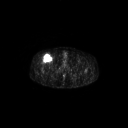
FDG PET of an extremity soft-tissue mass (from a PET/CT study), one axial slice. Slice 303 of 311 in the series (ordered by position). 3.27 mm slice thickness. 128 × 128 image matrix, field of view 700 × 700 mm. Male patient, age 56 years. Case-level facts recorded for this patient, not image findings: histological type: pleiomorphic leiomyosarcoma; grade: intermediate; site of the primary tumour: right thigh.
Outlined on this slice (expert contour drawn on MRI and transferred to this co-registered scan by the dataset authors):
- gross tumour volume including surrounding oedema: bounding box (x1, y1, x2, y2) in pixels: (41, 53, 51, 63)
- gross tumour volume (mass): (42, 55, 51, 63)